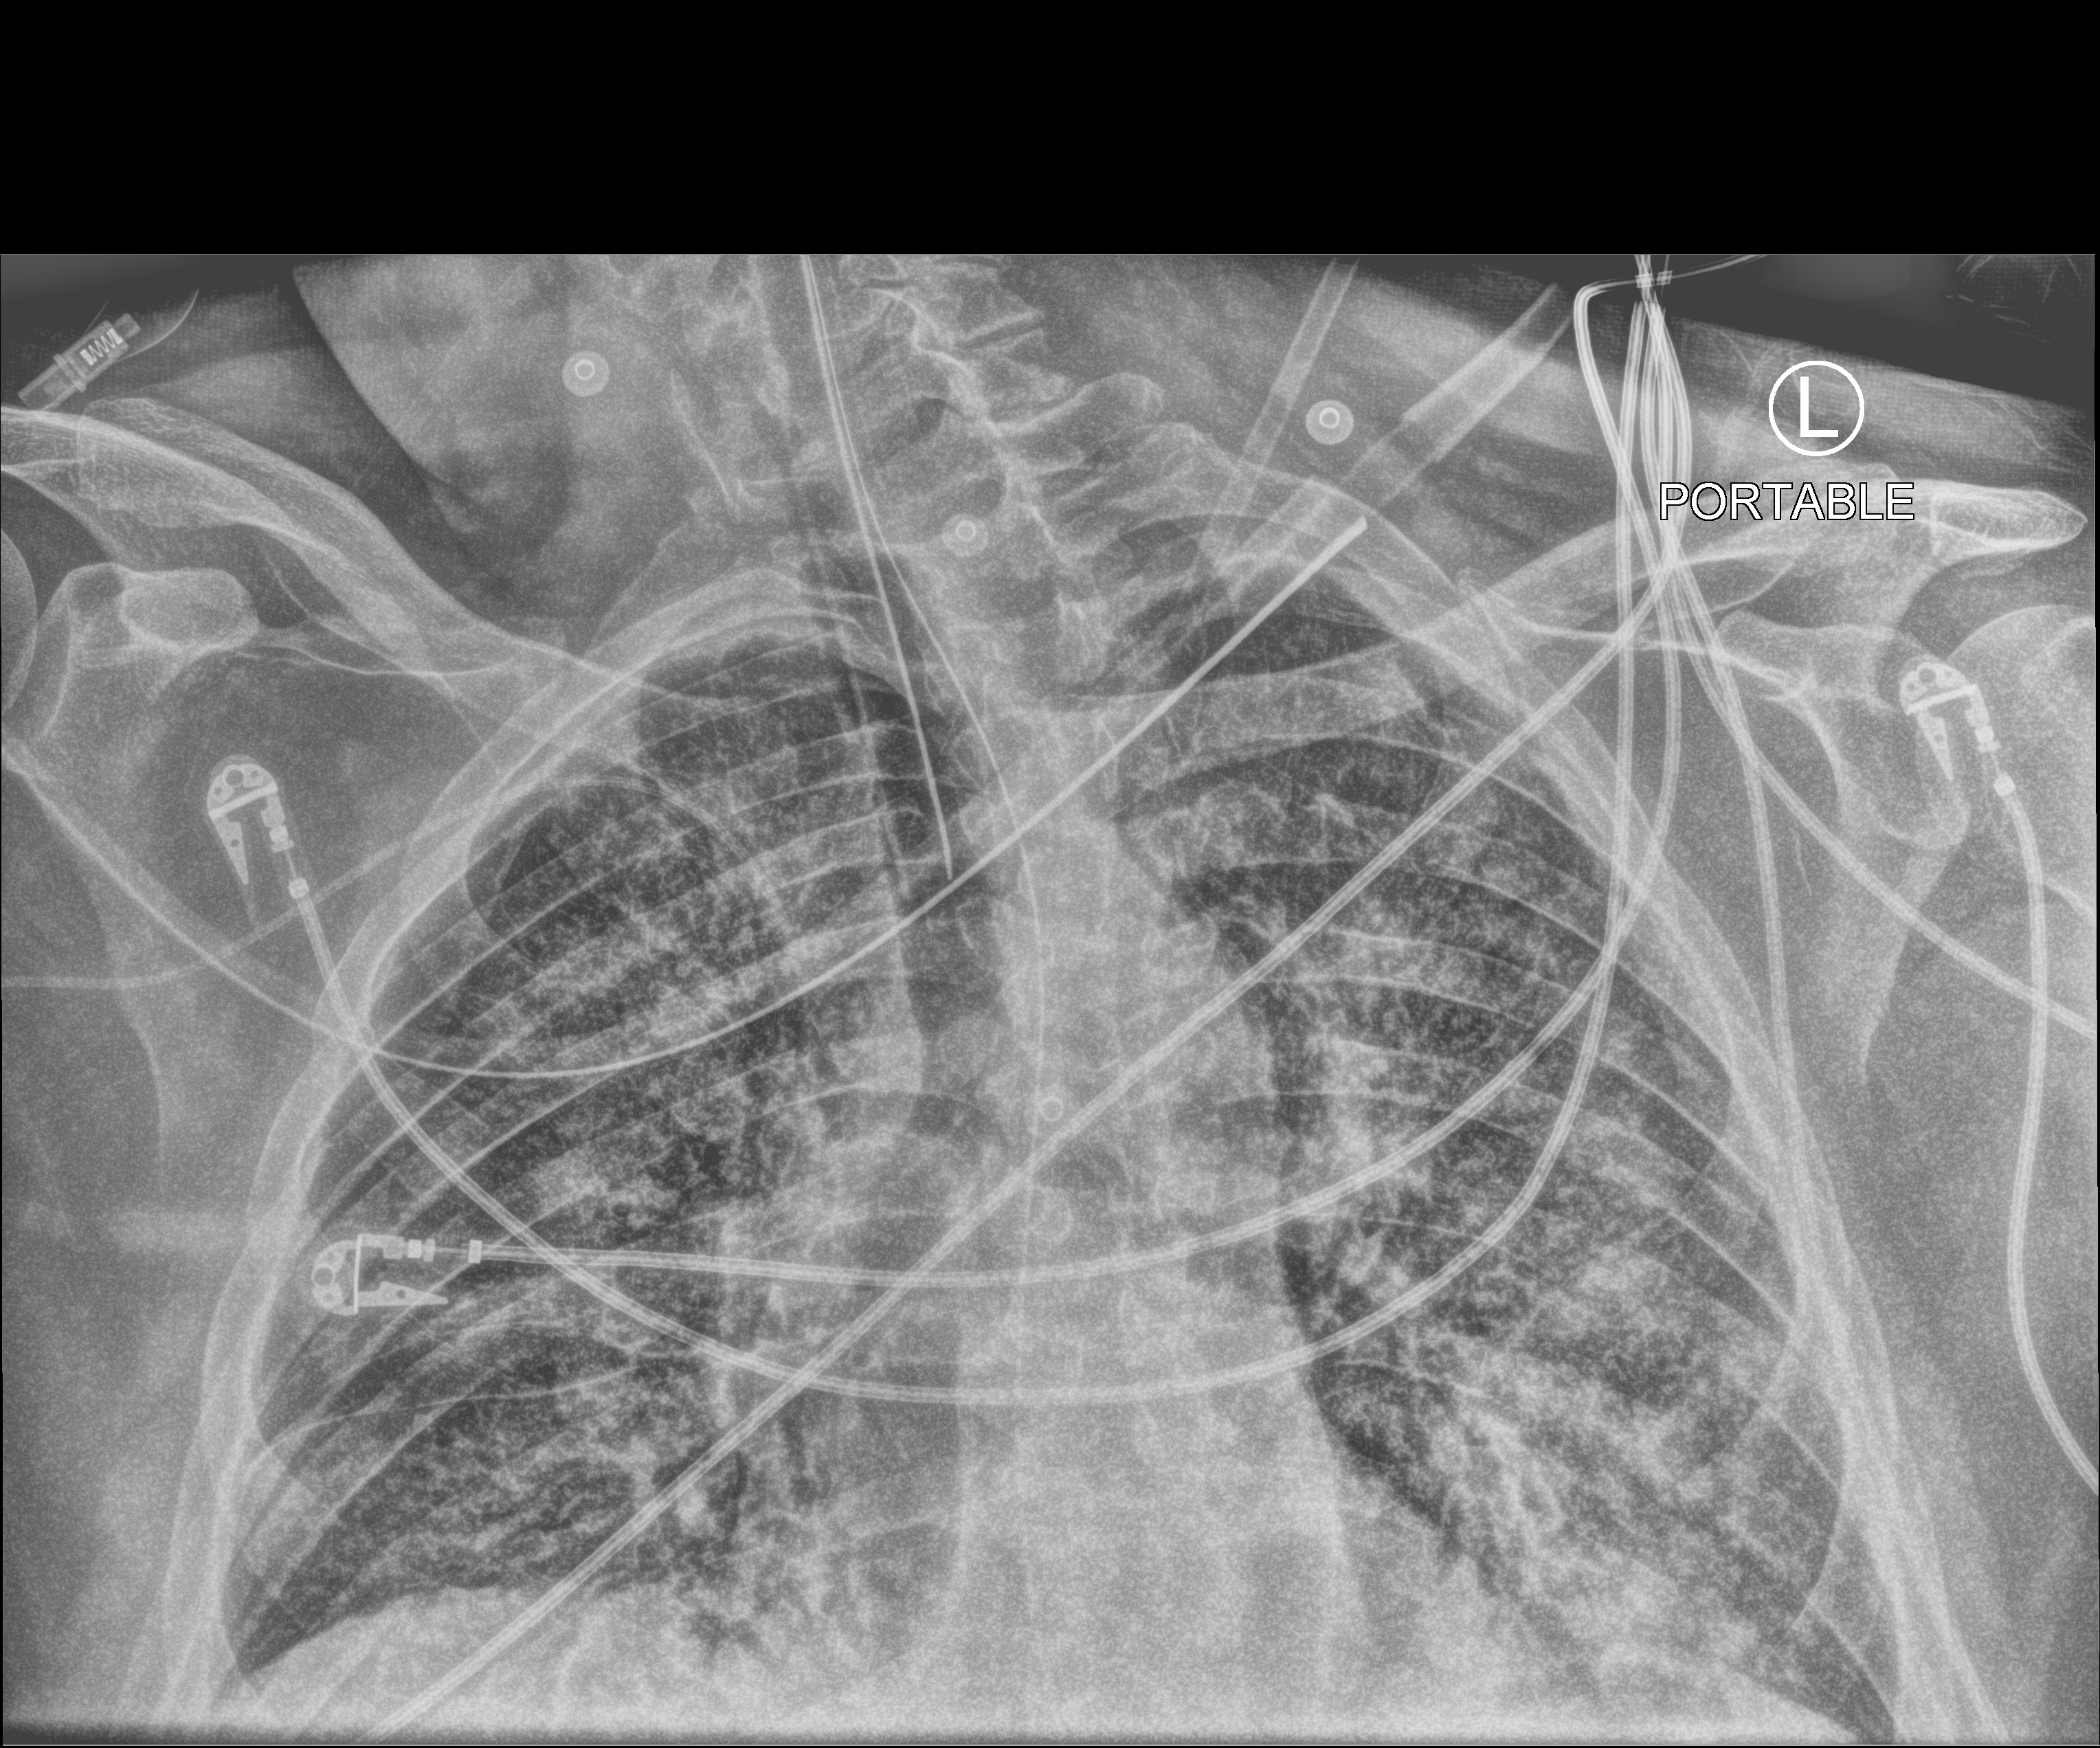
Chest X-ray (portable); anteroposterior (AP) projection. Male patient hospitalised with COVID-19, age 60–74 years.
From the hospital-stay record, not from the radiograph (when in the stay this image was taken is not recorded): admitted to intensive care during this hospital stay: yes; mechanically ventilated during this hospital stay: yes.